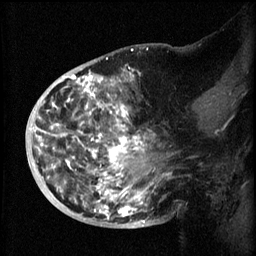
Breast MRI (dynamic contrast-enhanced), one sagittal slice; slice 28 of 60 in the series (ordered by position); 3 images stored at this slice position (order not interpretable as contrast timing); 1.5 T; TE 4.2 ms, TR 8.2 ms; 2 mm slice thickness; 256 × 256 image matrix, field of view 200 × 200 mm. Female patient, age 50 years.
Outlined on this slice (semi-automatic segmentation, software-assisted and operator-edited):
- analysis volume of interest (the breast-tissue region the enhancement analysis was run in; not a lesion): bounding box (x1, y1, x2, y2) in pixels: (44, 72, 173, 219)
- tumour enhancement mask (voxels above the 70 % enhancement threshold inside the analysis volume of interest): (44, 72, 154, 219)